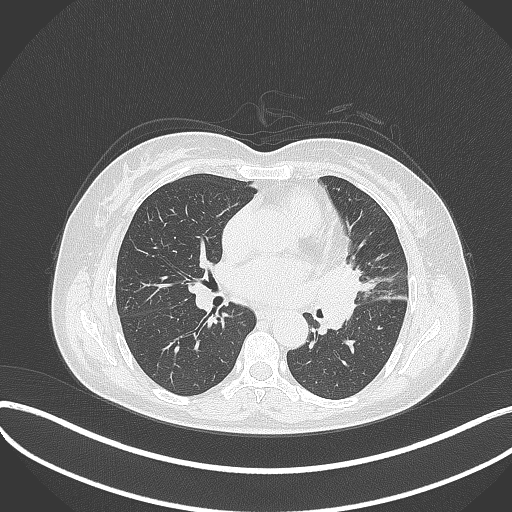
Chest CT, one axial slice; slice 180 of 373 in the series (ordered by position); reconstruction kernel B70f; lung window (W 1500 / L -600 HU); 1 mm slice thickness; 512 × 512 image matrix. Female patient, age 54 years. Case-level facts recorded for this patient, not image findings: clinical TNM (as recorded): T2a N1 M0.
Structures marked on this image (bounding box drawn by a radiologist):
- lung tumour (recorded histology: small cell carcinoma): box from (x=319, y=256) to (x=367, y=336) px